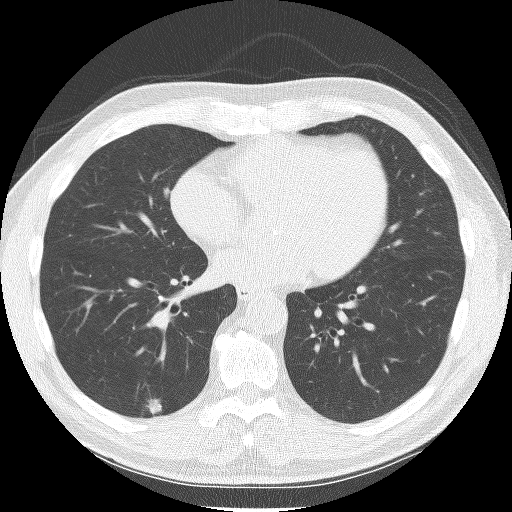
Axial slice from a low-dose chest CT screening exam; first (baseline) screen; lung window (W 1500 / L -600 HU); 2.5 mm slice thickness; 512 × 512 image matrix. Male participant, aged 61 years at enrolment. Current smoker at enrolment.
- Expert-annotated lung lesion, bounding box (x1, y1, x2, y2) in pixels: (128, 386, 175, 424).
- The exam's reader record, not a measurement of the box and not confirmed to be the same lesion: non-calcified nodule or mass ≥4 mm, right lower lobe, 12 × 11 mm, spiculated (stellate) margins, soft tissue attenuation.
- Official screen result: positive, change unspecified: nodule(s) >= 4 mm or enlarging nodule(s), mass(es), or other non-specific abnormalities suspicious for lung cancer.
- Lung cancer was diagnosed 232 days after this screen: adenocarcinoma, NOS, right lower lobe, moderately differentiated (G2), stage IA (AJCC 6th edition), 9 mm at pathology.